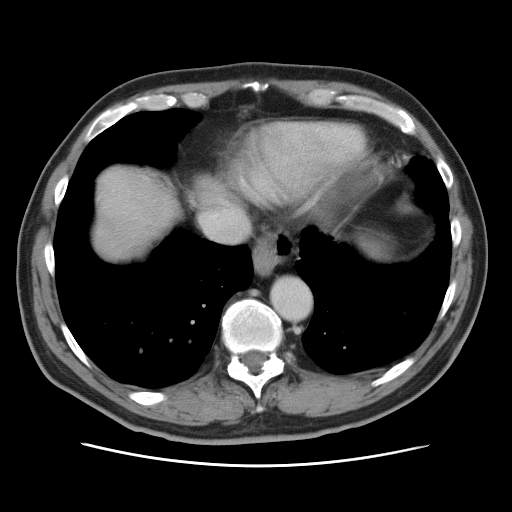
Contrast-enhanced abdominal CT, one axial slice. Slice 72 of 80 in the series (ordered by position). 120 kVp. Intravenous contrast given. Soft-tissue window (W 400 / L 40 HU). 5 mm slice thickness. 512 × 512 image matrix, field of view 370 × 370 mm. Male patient, age 69 years. Case-level facts recorded for this patient, not image findings: diagnosis: colorectal cancer liver metastases, imaged before liver resection; multiple liver metastases: no; largest metastasis: 5 cm; disease in both lobes: yes.
Annotated regions visible in this slice (expert manual segmentation):
- hepatic veins: bounding box [x1, y1, x2, y2] px = [119, 185, 243, 239]
- liver: [93, 169, 172, 256]
- planned liver remnant (the part of the liver to remain after resection): [92, 212, 160, 257]